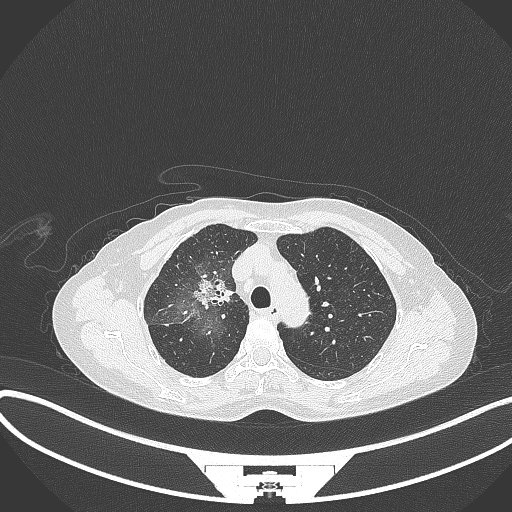
Chest CT, one axial slice. Slice 234 of 284 in the series (ordered by position). Reconstruction kernel B70f. Lung window (W 1500 / L -600 HU). 512 × 512 image matrix. Female patient, age 59 years. Case-level facts recorded for this patient, not image findings: clinical TNM (as recorded): T3 N0 M0.
Outlined on this slice (rectangle marked by the reading radiologist):
- lung tumour (recorded histology: adenocarcinoma): bounding box [x1, y1, x2, y2] px = [192, 273, 235, 316]